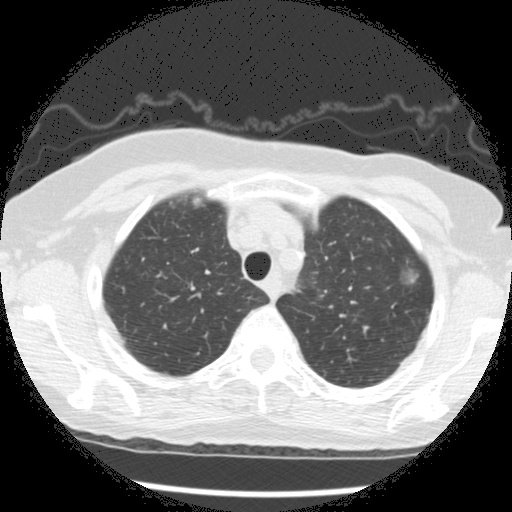
Axial slice from a low-dose chest CT screening exam; second screening round (one year after baseline); lung window (W 1500 / L -600 HU); 2.5 mm slice thickness; standard (soft-tissue) reconstruction kernel (STANDARD); slice 39 of 266 in the series; 512 × 512 image matrix. Female, age 73 years at enrolment. Former smoker at enrolment.
Expert-annotated lung lesion, bounding box [x1, y1, x2, y2] px = [391, 246, 433, 289]. The screening reader recorded 3 non-calcified nodules or masses ≥4 mm on this exam; which of them this box marks is not recorded. Official screen result: positive, change unspecified: nodule(s) >= 4 mm or enlarging nodule(s), mass(es), or other non-specific abnormalities suspicious for lung cancer. Lung cancer was diagnosed 49 days after this screen: bronchiolo-alveolar adenocarcinoma, NOS, left upper lobe, well differentiated (G1), stage IA (AJCC 6th edition), 10 mm at pathology.